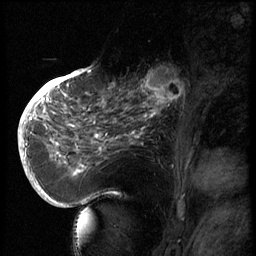
Breast MRI (dynamic contrast-enhanced), one sagittal slice. Position 29 of 66 along the scan axis. 3 images stored at this slice position (order not interpretable as contrast timing). 1.5 T. TE 4.2 ms, TR 8.9 ms. 2.5 mm slice thickness. 256 × 256 image matrix, field of view 200 × 200 mm. Patient: female, 56 years. Case-level facts recorded for this patient, not image findings: setting: breast cancer imaged before/during neoadjuvant chemotherapy.
Structures marked on this image (semi-automatic segmentation, software-assisted and operator-edited):
- analysis volume of interest (the breast-tissue region the enhancement analysis was run in; not a lesion): bounding box [x1, y1, x2, y2] px = [129, 62, 194, 127]
- tumour enhancement mask (voxels above the 140 % enhancement threshold inside the analysis volume of interest): [138, 66, 187, 121]